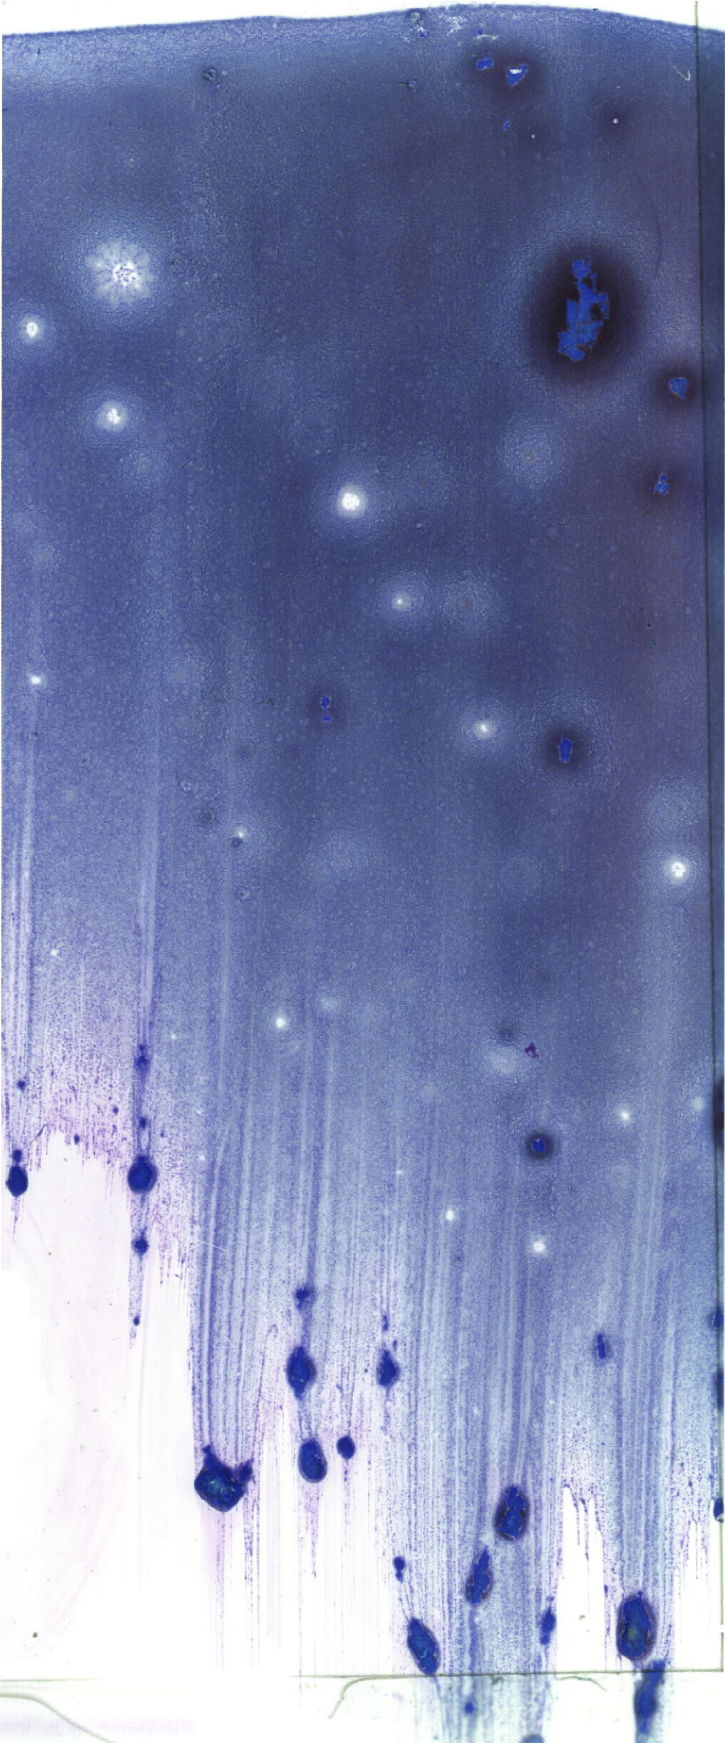
Bone marrow aspirate smear, May-Grünwald-Giemsa (MGG) stain, whole-slide image, a low-resolution overview of the entire scanned area, about 20.6 x 49.4 mm. Female patient.
Diagnosis: Acute Myeloid Leukemia with Maturation.